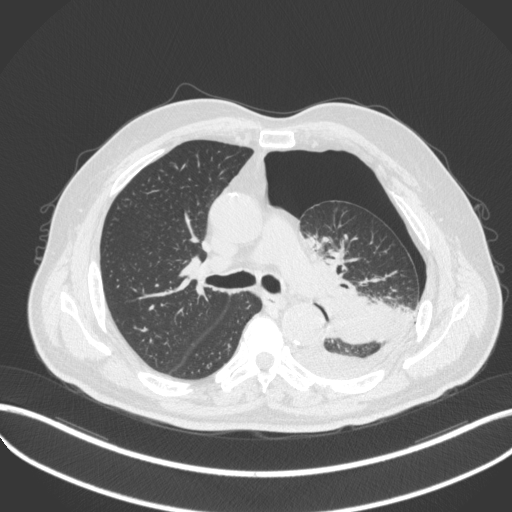
Chest CT, one axial slice; slice 326 of 466 in the series (ordered by position); lung window (W 1500 / L -600 HU); 1 mm slice thickness; 512 × 512 image matrix, field of view 400 × 400 mm. Patient: male, 76 years. From the clinical record (not read from this slice): clinical TNM (as recorded): T3 N0 M1b.
Outlined on this slice (rectangle marked by the reading radiologist):
- lung tumour (recorded histology: adenocarcinoma): bounding box <323,292,387,344> (left, top, right, bottom; pixels)